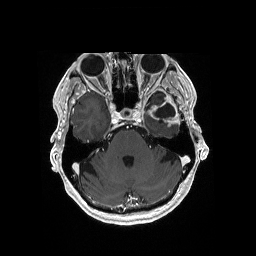
Brain MRI from a brain-tumour surgery series, one axial slice; position 127 of 176 along the scan axis; T1-weighted post-contrast; 1 mm slice thickness; 256 × 256 image matrix, field of view 256 × 256 mm. Case-level facts recorded for this patient, not image findings: histopathology: Glioblastoma; WHO grade: 4; IDH mutation: no; tumour location: Left Medial Temporal.
Outlined on this slice (outlined manually by an expert reader):
- previous resection cavity: bounding box (x1, y1, x2, y2) in pixels: (154, 103, 176, 118)
- tumour: (151, 114, 180, 128)